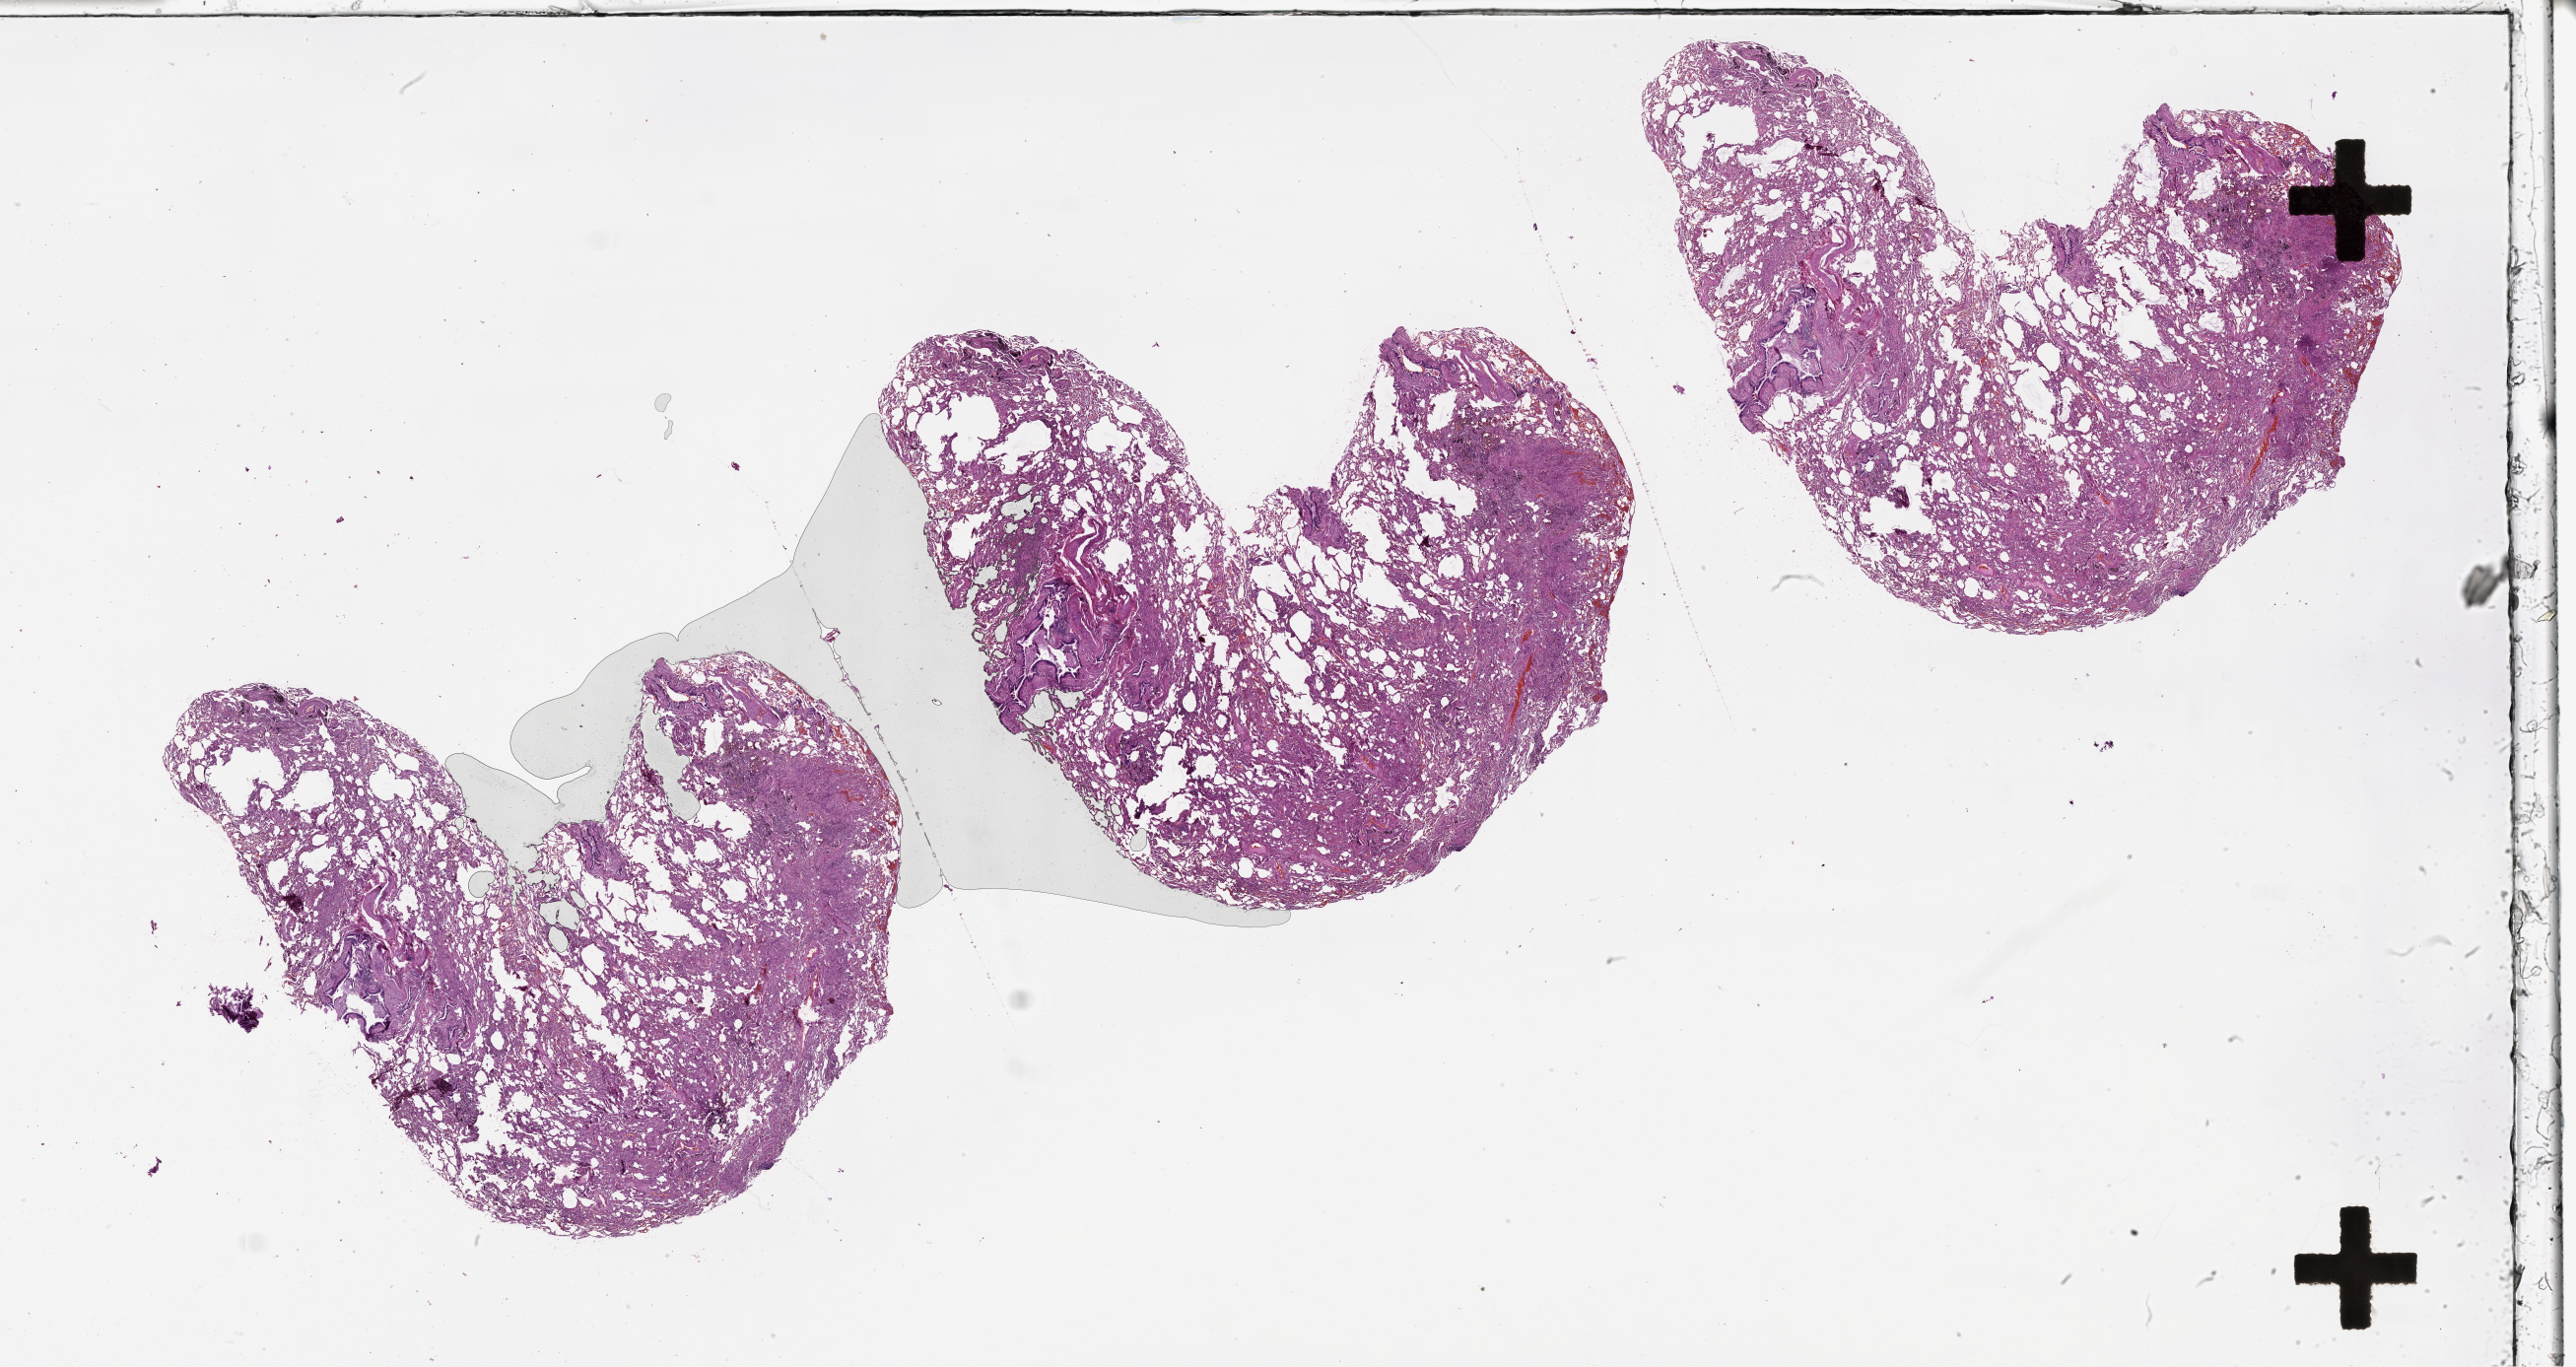
Hematoxylin and eosin (H&E) stained whole-slide image — shown as a low-resolution overview of the whole scanned area (about 42.1 x 22.3 mm), lung, normal (non-tumour) tissue. Male, 53 y/o.
* this section: normal (non-tumour) tissue from the same patient
* patient diagnosis (cohort enrolment): squamous cell carcinoma (lung)